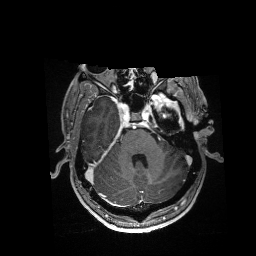
Brain MRI from a brain-tumour surgery series, one axial slice. Slice 116 of 176 in the series (ordered by position). T1-weighted post-contrast. 1 mm slice thickness. 256 × 256 image matrix, field of view 256 × 256 mm. Case-level facts recorded for this patient, not image findings: histopathology: Glioblastoma; WHO grade: 4; IDH mutation: no; tumour location: Left Anterior/Superior Temporal.
Structures marked on this image (outlined manually by an expert reader):
- residual tumour: bounding box [x1, y1, x2, y2] px = [152, 93, 180, 113]